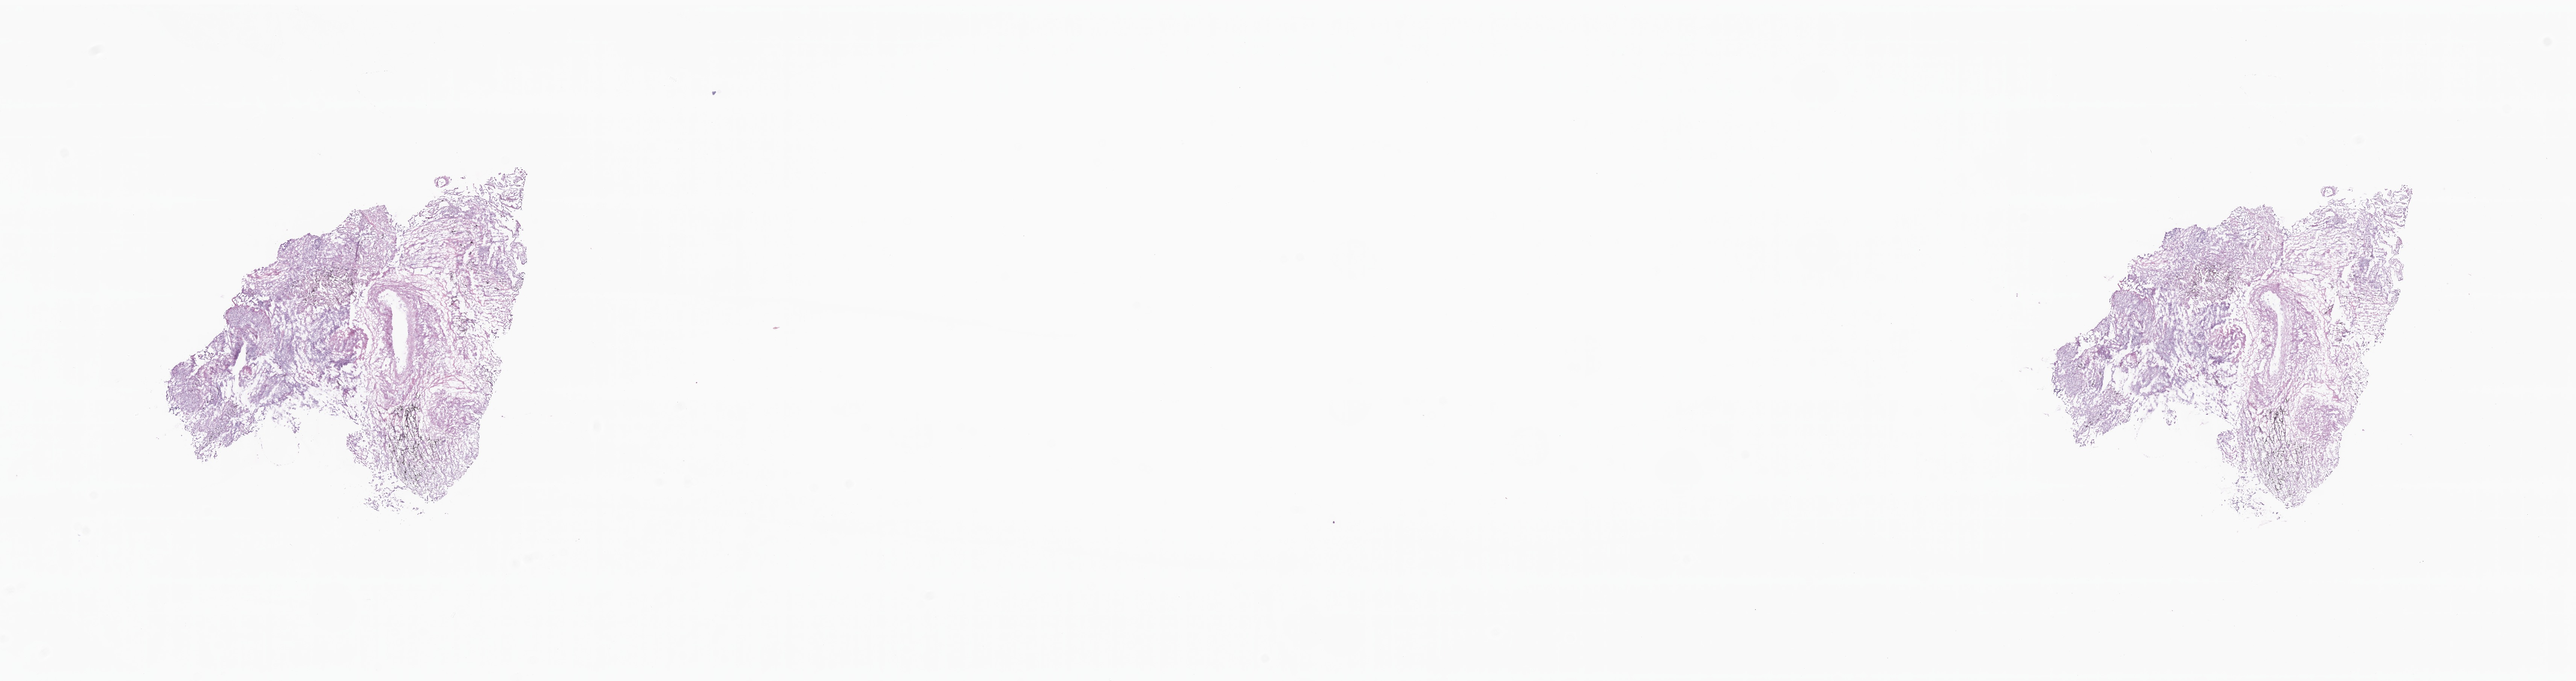
Haematoxylin and eosin whole-slide image — shown as a low-resolution overview of the whole scanned area (about 28.9 x 7.6 mm). Cryosection. Specimen: primary tumor. Anatomic site: upper lobe of left lung. Patient: female, age at initial diagnosis 83 years. Pathologist review of this section (percent, as recorded): tumor cells 20%, tumor nuclei 20%, stromal cells 0%, necrosis 5%, normal cells 75%. Inflammatory infiltration, as recorded: lymphocyte infiltration 0%, monocyte infiltration 0%, neutrophil infiltration 0%.
* diagnosis: Squamous cell carcinoma, NOS
* section: top of the tissue portion